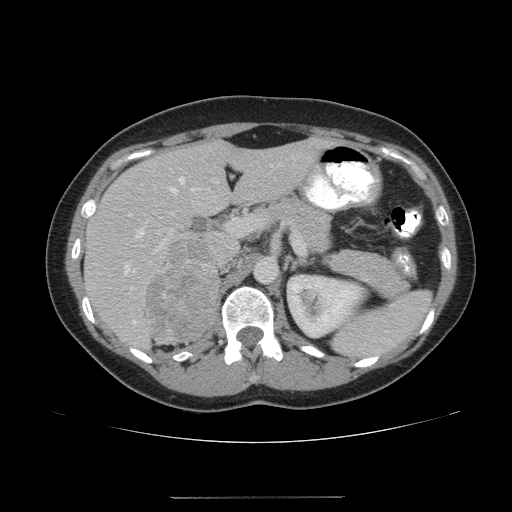
Contrast-enhanced abdominal CT, one axial slice. Slice 111 of 161 in the series (ordered by position). Reconstruction kernel STANDARD. 120 kVp. Intravenous contrast given. Soft-tissue window (W 400 / L 40 HU). 3.75 mm slice thickness. 512 × 512 image matrix. Female patient. From the clinical record (not read from this slice): diagnosis: adrenocortical carcinoma; tumour side: right adrenal; tumour size at pathology: 9 cm; Ki-67 index: 14 %; stage (as recorded): 3.
Structures marked on this image (semi-automatic segmentation, software-assisted and operator-edited):
- mass: bounding box <146,242,217,343> (left, top, right, bottom; pixels)